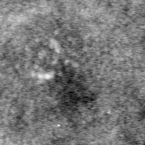
Cropped region of a digitized screen-film mammogram centred on a radiologist-marked abnormality; right breast; MLO view.
Marked abnormality: calcifications, morphology pleomorphic, distribution clustered; BI-RADS assessment category 3; pathology (as recorded): benign.